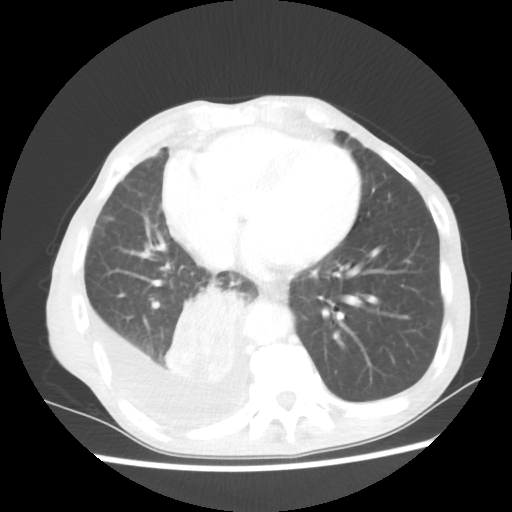
Chest CT, one axial slice. Position 21 of 60 along the scan axis. 80 kVp. Lung window (W 1500 / L -600 HU). 5 mm slice thickness. 512 × 512 image matrix. Male patient, age 76 years. Case-level facts recorded for this patient, not image findings: clinical TNM (as recorded): T3 N3 M1a.
Annotated regions visible in this slice (bounding box drawn by a radiologist):
- lung tumour (recorded histology: squamous cell carcinoma): bounding box <158,278,253,386> (left, top, right, bottom; pixels)